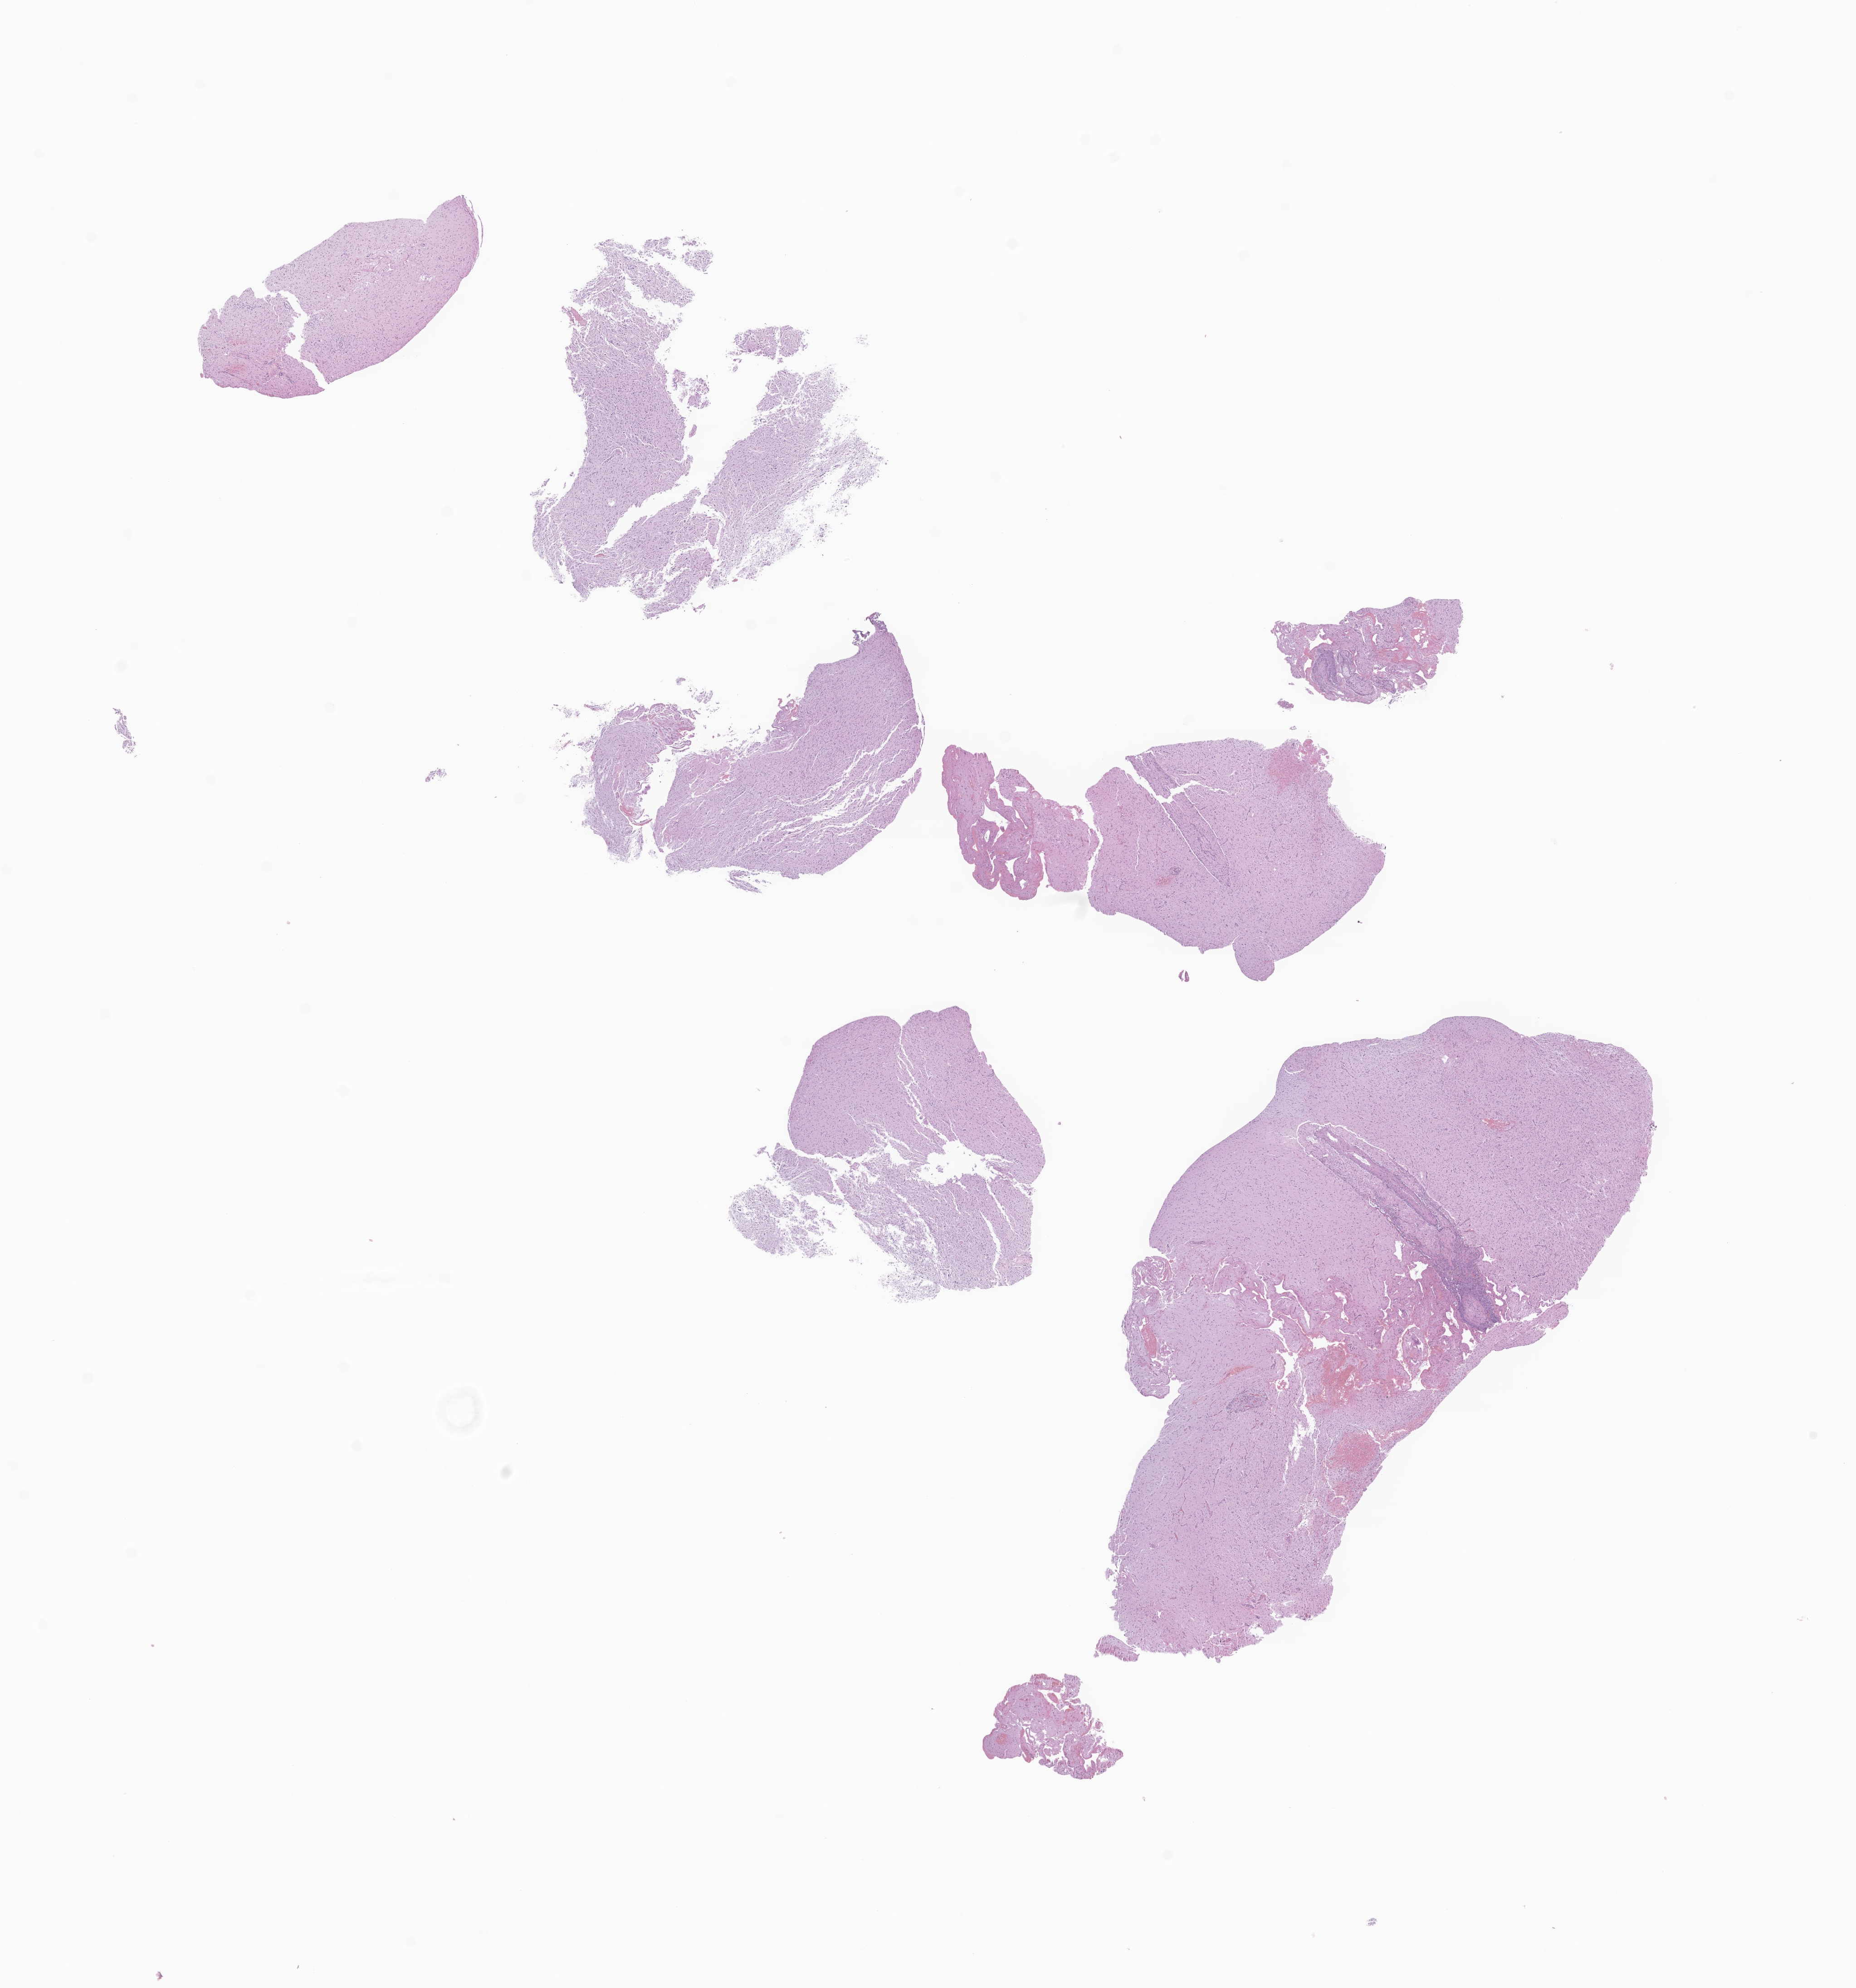
Haematoxylin and eosin whole-slide image of tumor tissue from the brain — a low-resolution overview of the entire scanned area, about 17.3 x 18.5 mm. FFPE section. Patient female; age 222 months.
Recorded diagnosis: Neoplasm, uncertain whether benign or malignant.